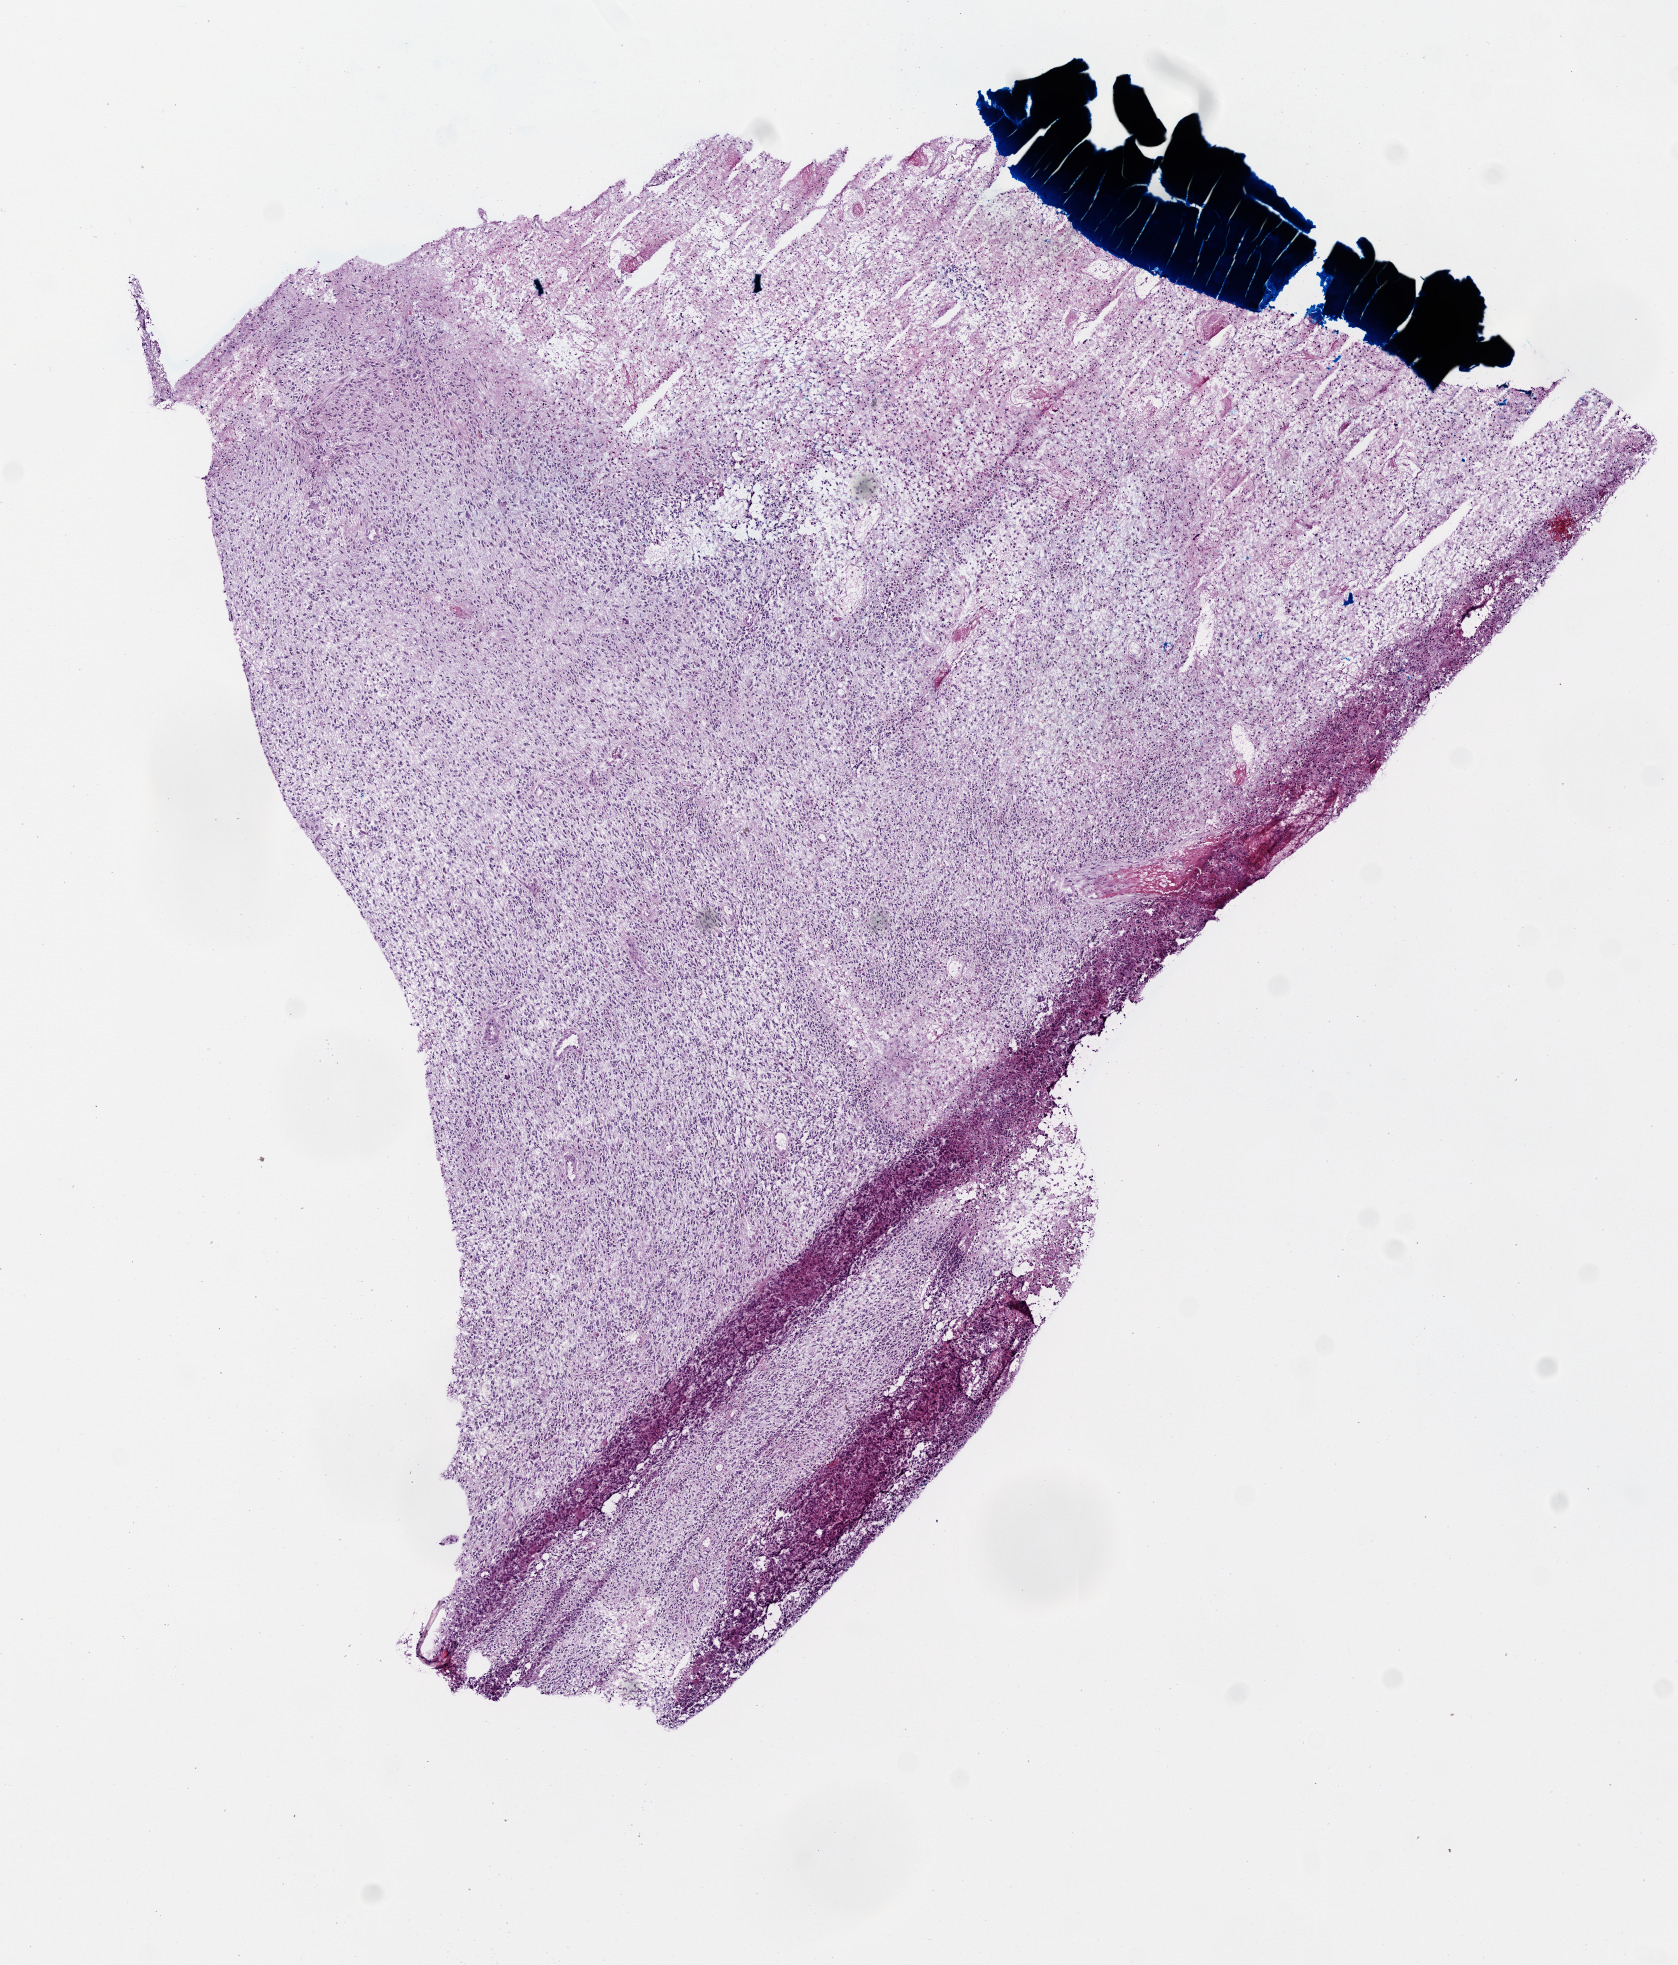
H&E whole-slide image — shown as a low-resolution overview of the whole scanned area (about 6.8 x 7.9 mm, from a 20x scan); frozen section; sample: primary tumour, brain. Female, age 76 years at initial diagnosis. Pathologist review of this section (percent, as recorded): tumour cells 80%, tumour nuclei 90%, normal cells 0%, stromal cells 5%, necrosis 15%.
Pathologic diagnosis: Glioblastoma.